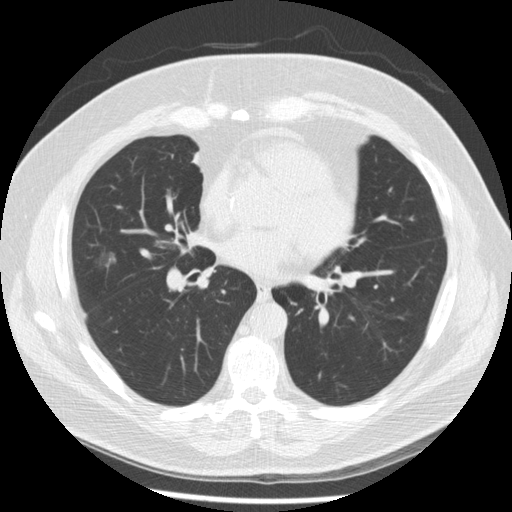
Axial slice from a low-dose chest CT screening exam; second annual screen; lung window (W 1500 / L -600 HU); 2.5 mm slice thickness; slice 122 of 230 in the series; 512 × 512 image matrix. Male participant, aged 67 years at enrolment. Former smoker at enrolment.
• Lesion marked by an expert reader, bounding box (x1, y1, x2, y2) in pixels: (75, 243, 126, 288).
• The exam's reader record, not a measurement of the box and not confirmed to be the same lesion: non-calcified nodule or mass ≥4 mm, right middle lobe, 19 × 16 mm, smooth margins, soft tissue attenuation, pre-existing on the prior screen: yes; interval growth: yes.
• Later outcome: lung cancer diagnosed 47 days after this screen — adenocarcinoma, NOS, right middle lobe, moderately differentiated (G2), stage IA (AJCC 6th edition), 14 mm at pathology.